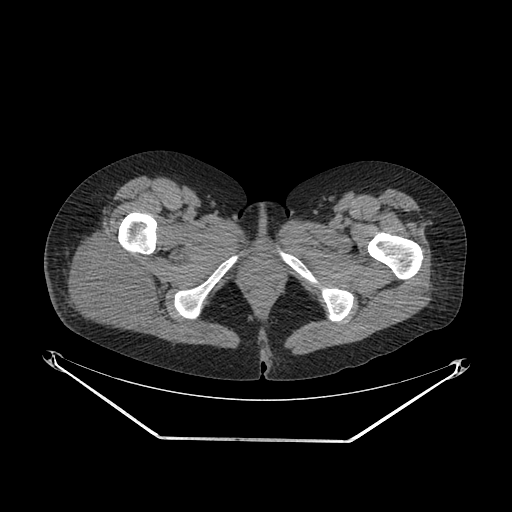
CT of an extremity soft-tissue mass (from a PET/CT study), one axial slice. Soft-tissue window (W 400 / L 40 HU). 512 × 512 image matrix, field of view 500 × 500 mm. Female patient. From the clinical record (not read from this slice): histological type: epithelioid sarcoma with vascular differentiation; site of the primary tumour: right buttock.
Annotated regions visible in this slice (expert contour drawn on MRI and transferred to this co-registered scan by the dataset authors):
- gross tumour volume (mass): bounding box [x1, y1, x2, y2] px = [66, 237, 154, 328]